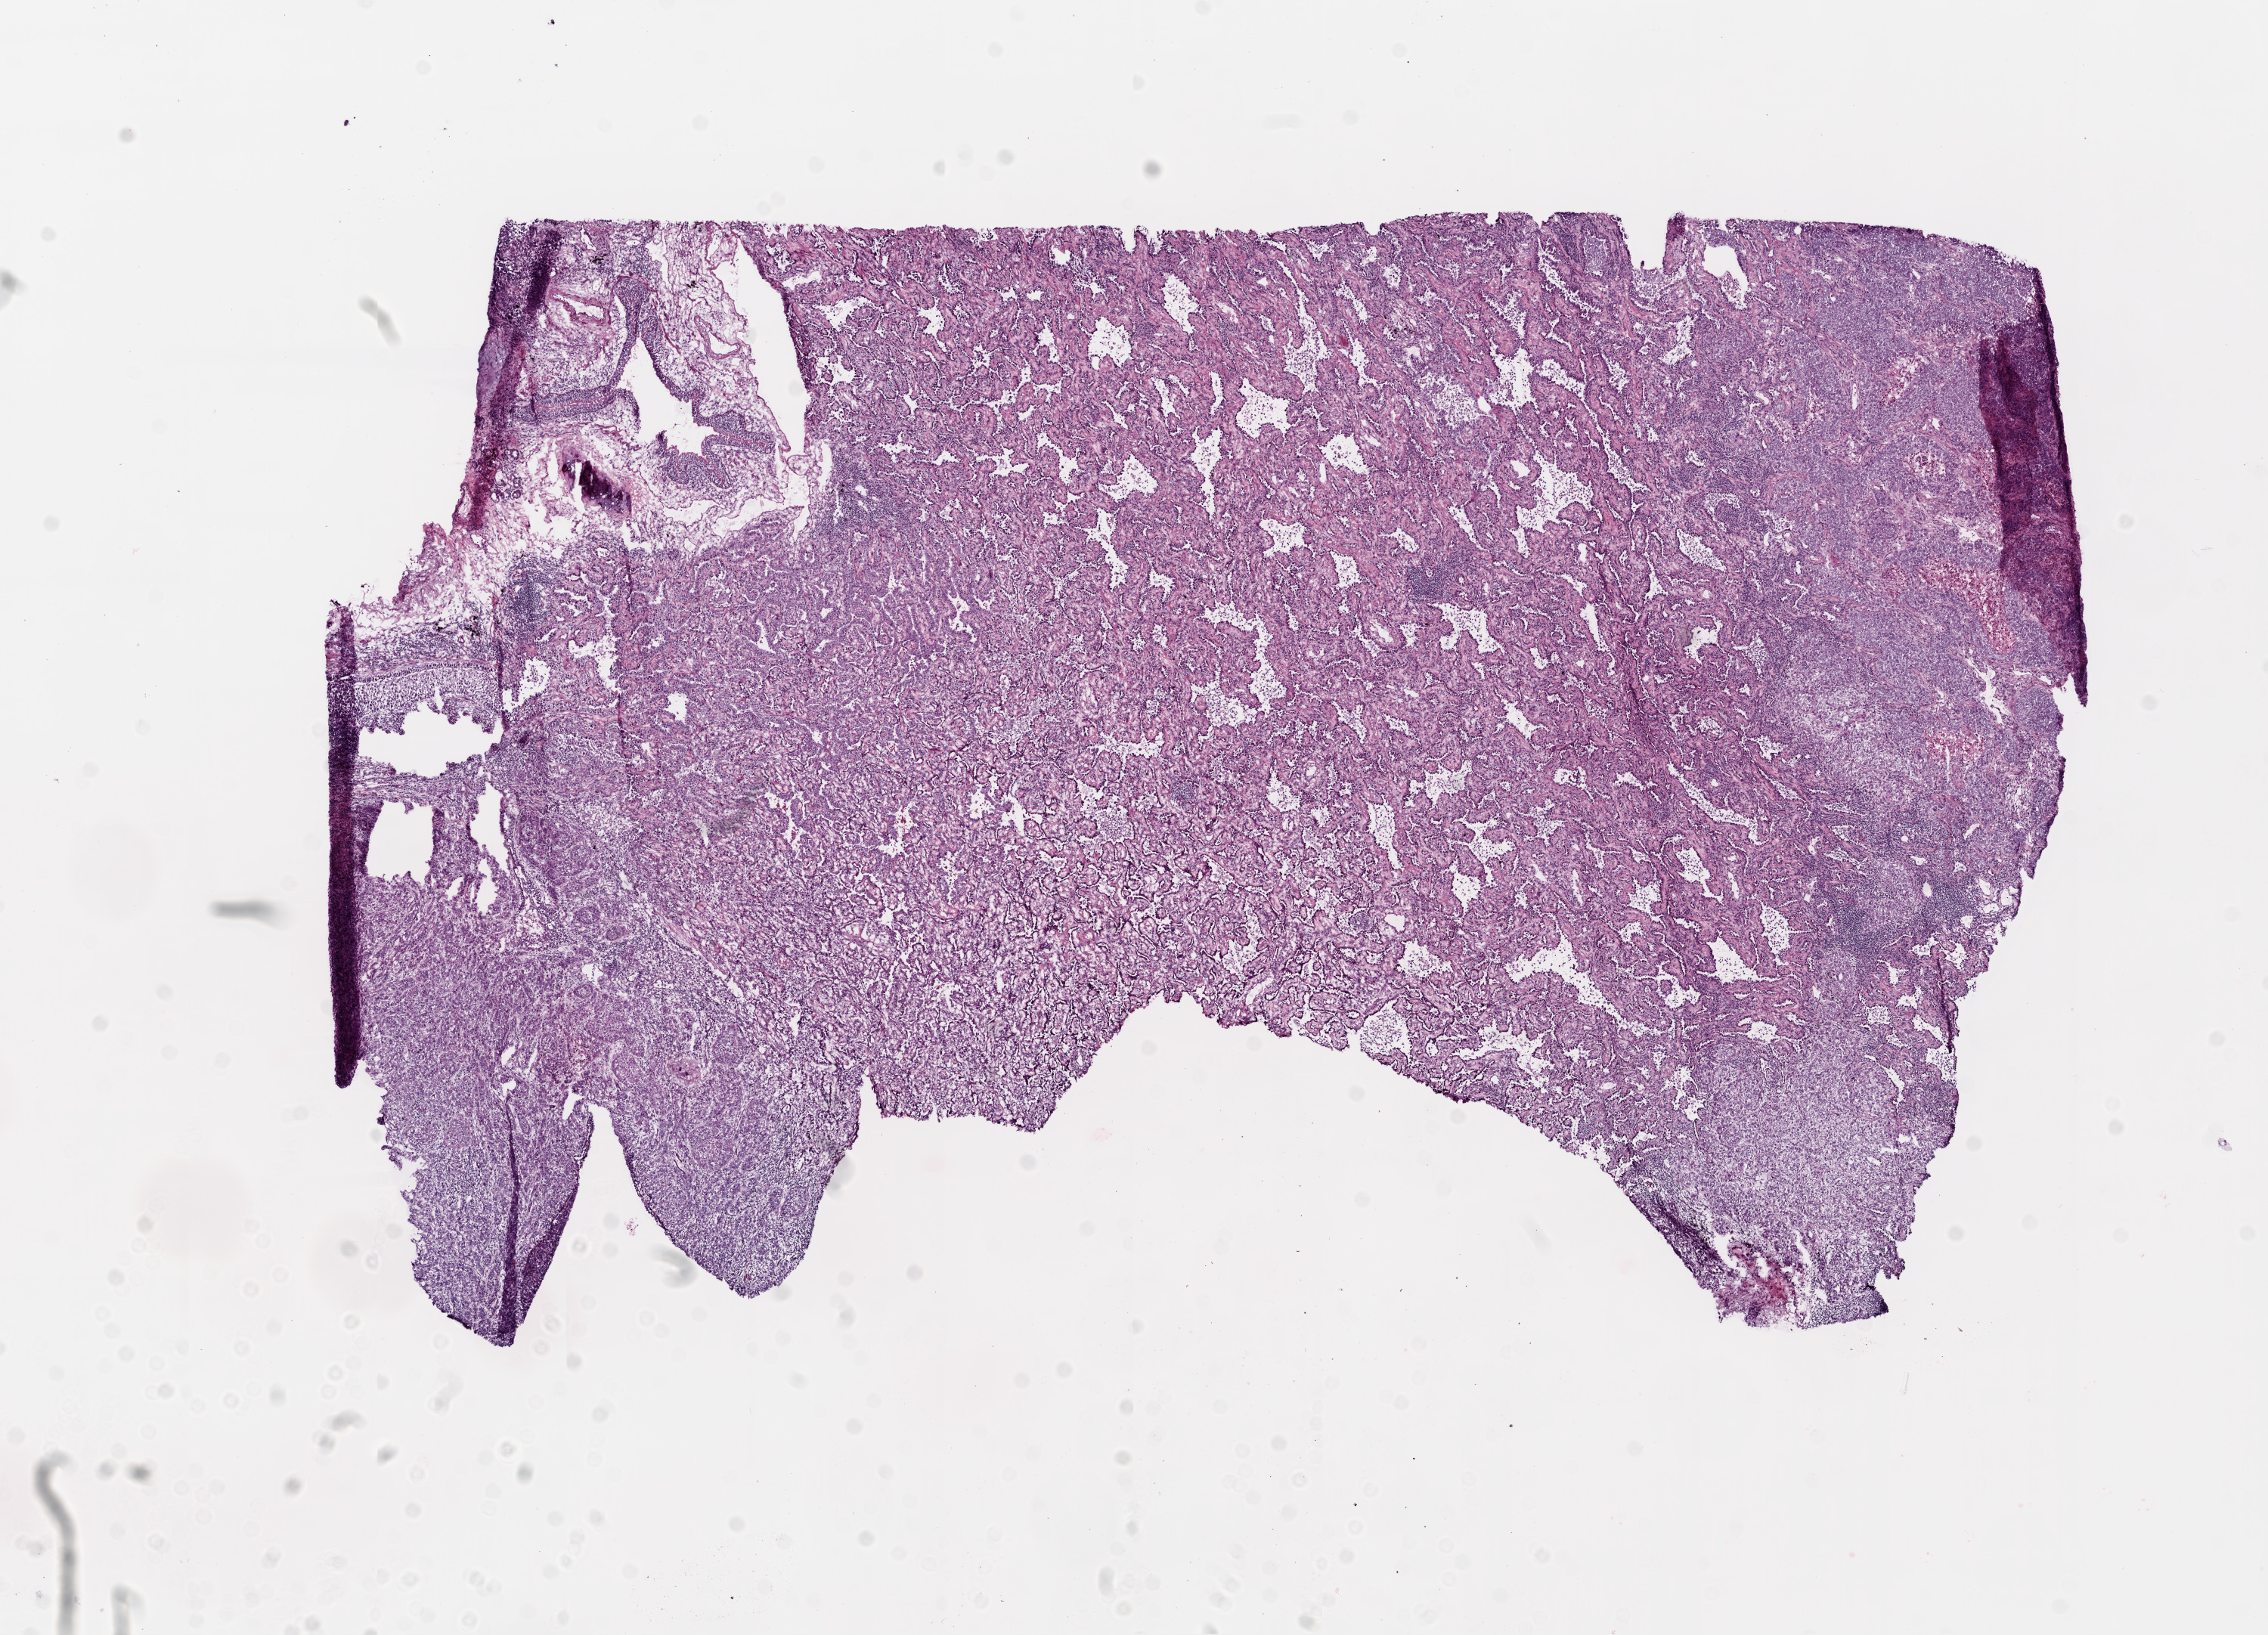
H&E-stained whole-slide image — shown as a low-resolution overview of the whole scanned area (about 12.0 x 8.7 mm, slide scanned at 20x), frozen section from the top of the tissue portion, lung, primary tumour sample. Female patient; age at initial diagnosis 67 years. Slide review estimates, as recorded: tumour cells 63%, tumour nuclei 75%, normal cells 2%, stromal cells 30%, necrosis 5%.
AJCC pathologic stage: IV (6th edition). TNM: T4 N1 M1. Diagnosis: Adenocarcinoma with mixed subtypes (lower lobe, lung).